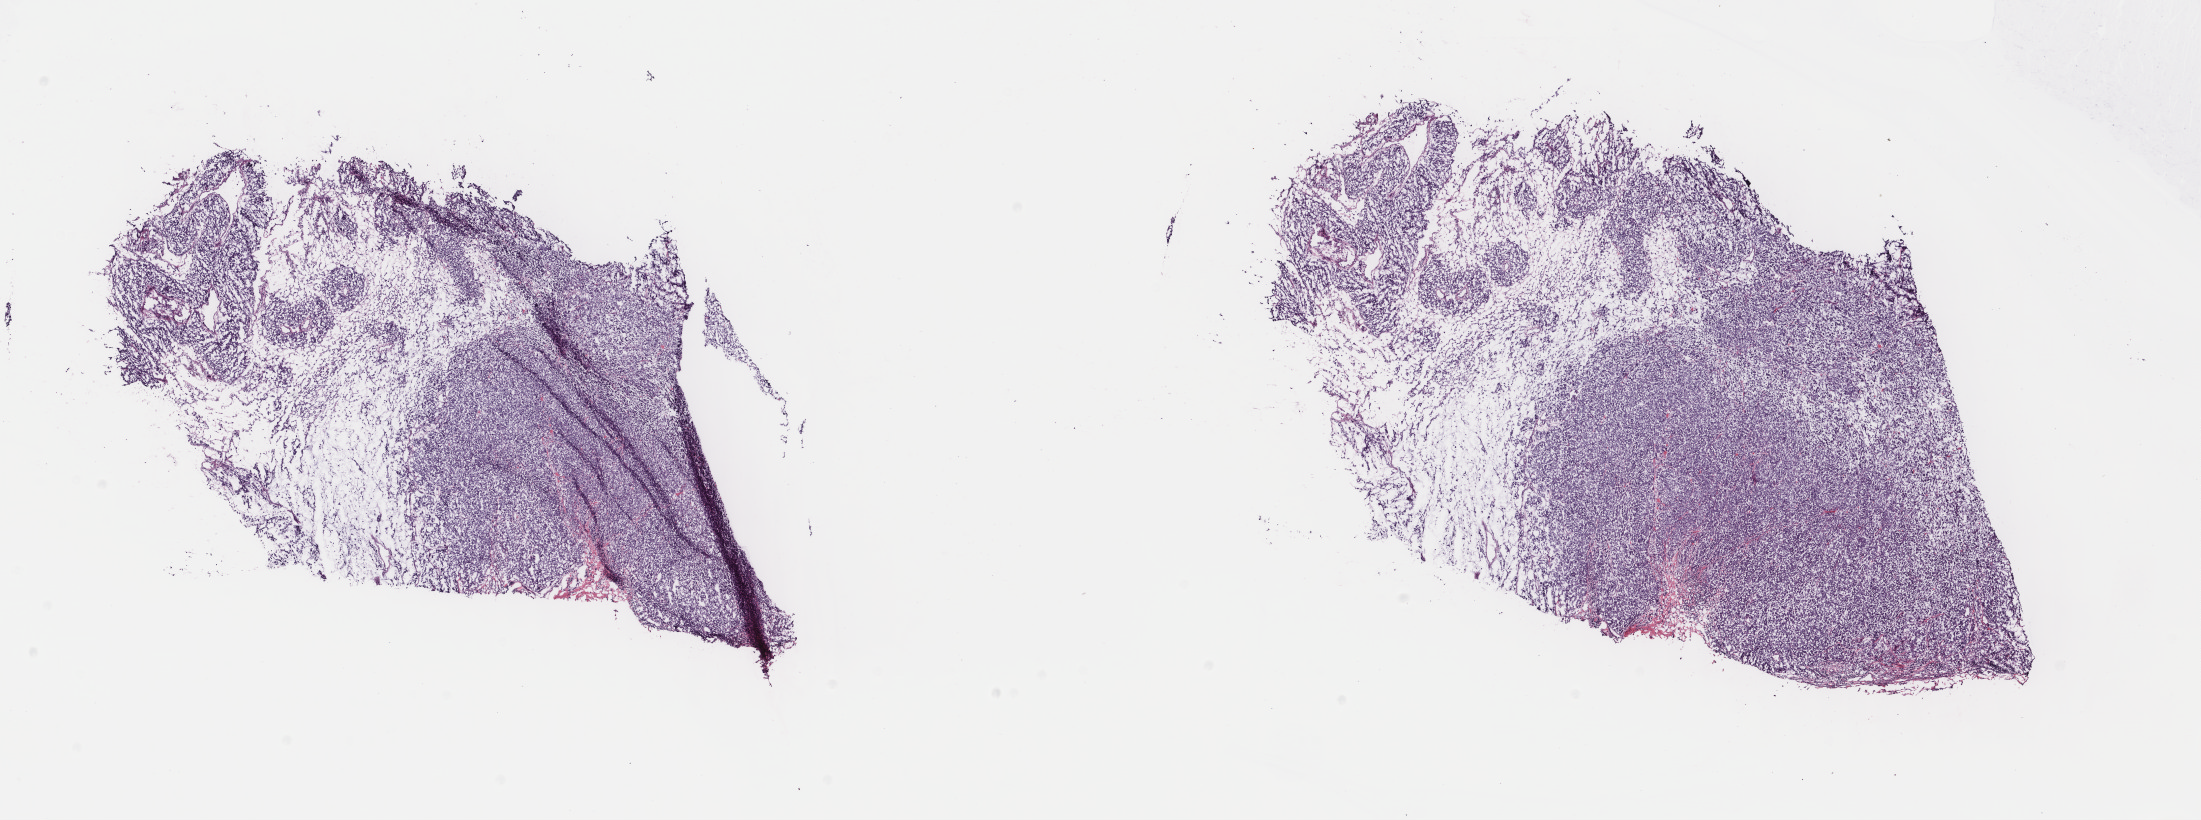
Digitized Hematoxylin and eosin (H&E) stained tissue section (whole slide) — whole scanned area (about 17.5 x 6.5 mm, from a 40x scan) shown as a low-resolution overview. Frozen section. Metastatic tumour sample. Female patient; age at initial diagnosis 28 years. Composition of this section per pathologist review: tumour cells 100%, tumour nuclei 95%, normal cells 0%, stromal cells 0%, necrosis 0%. Infiltration values recorded for this section: lymphocyte infiltration 0%, monocyte infiltration 0%, neutrophil infiltration 0%.
This section: metastatic tumour tissue. Patient diagnosis: Amelanotic melanoma.